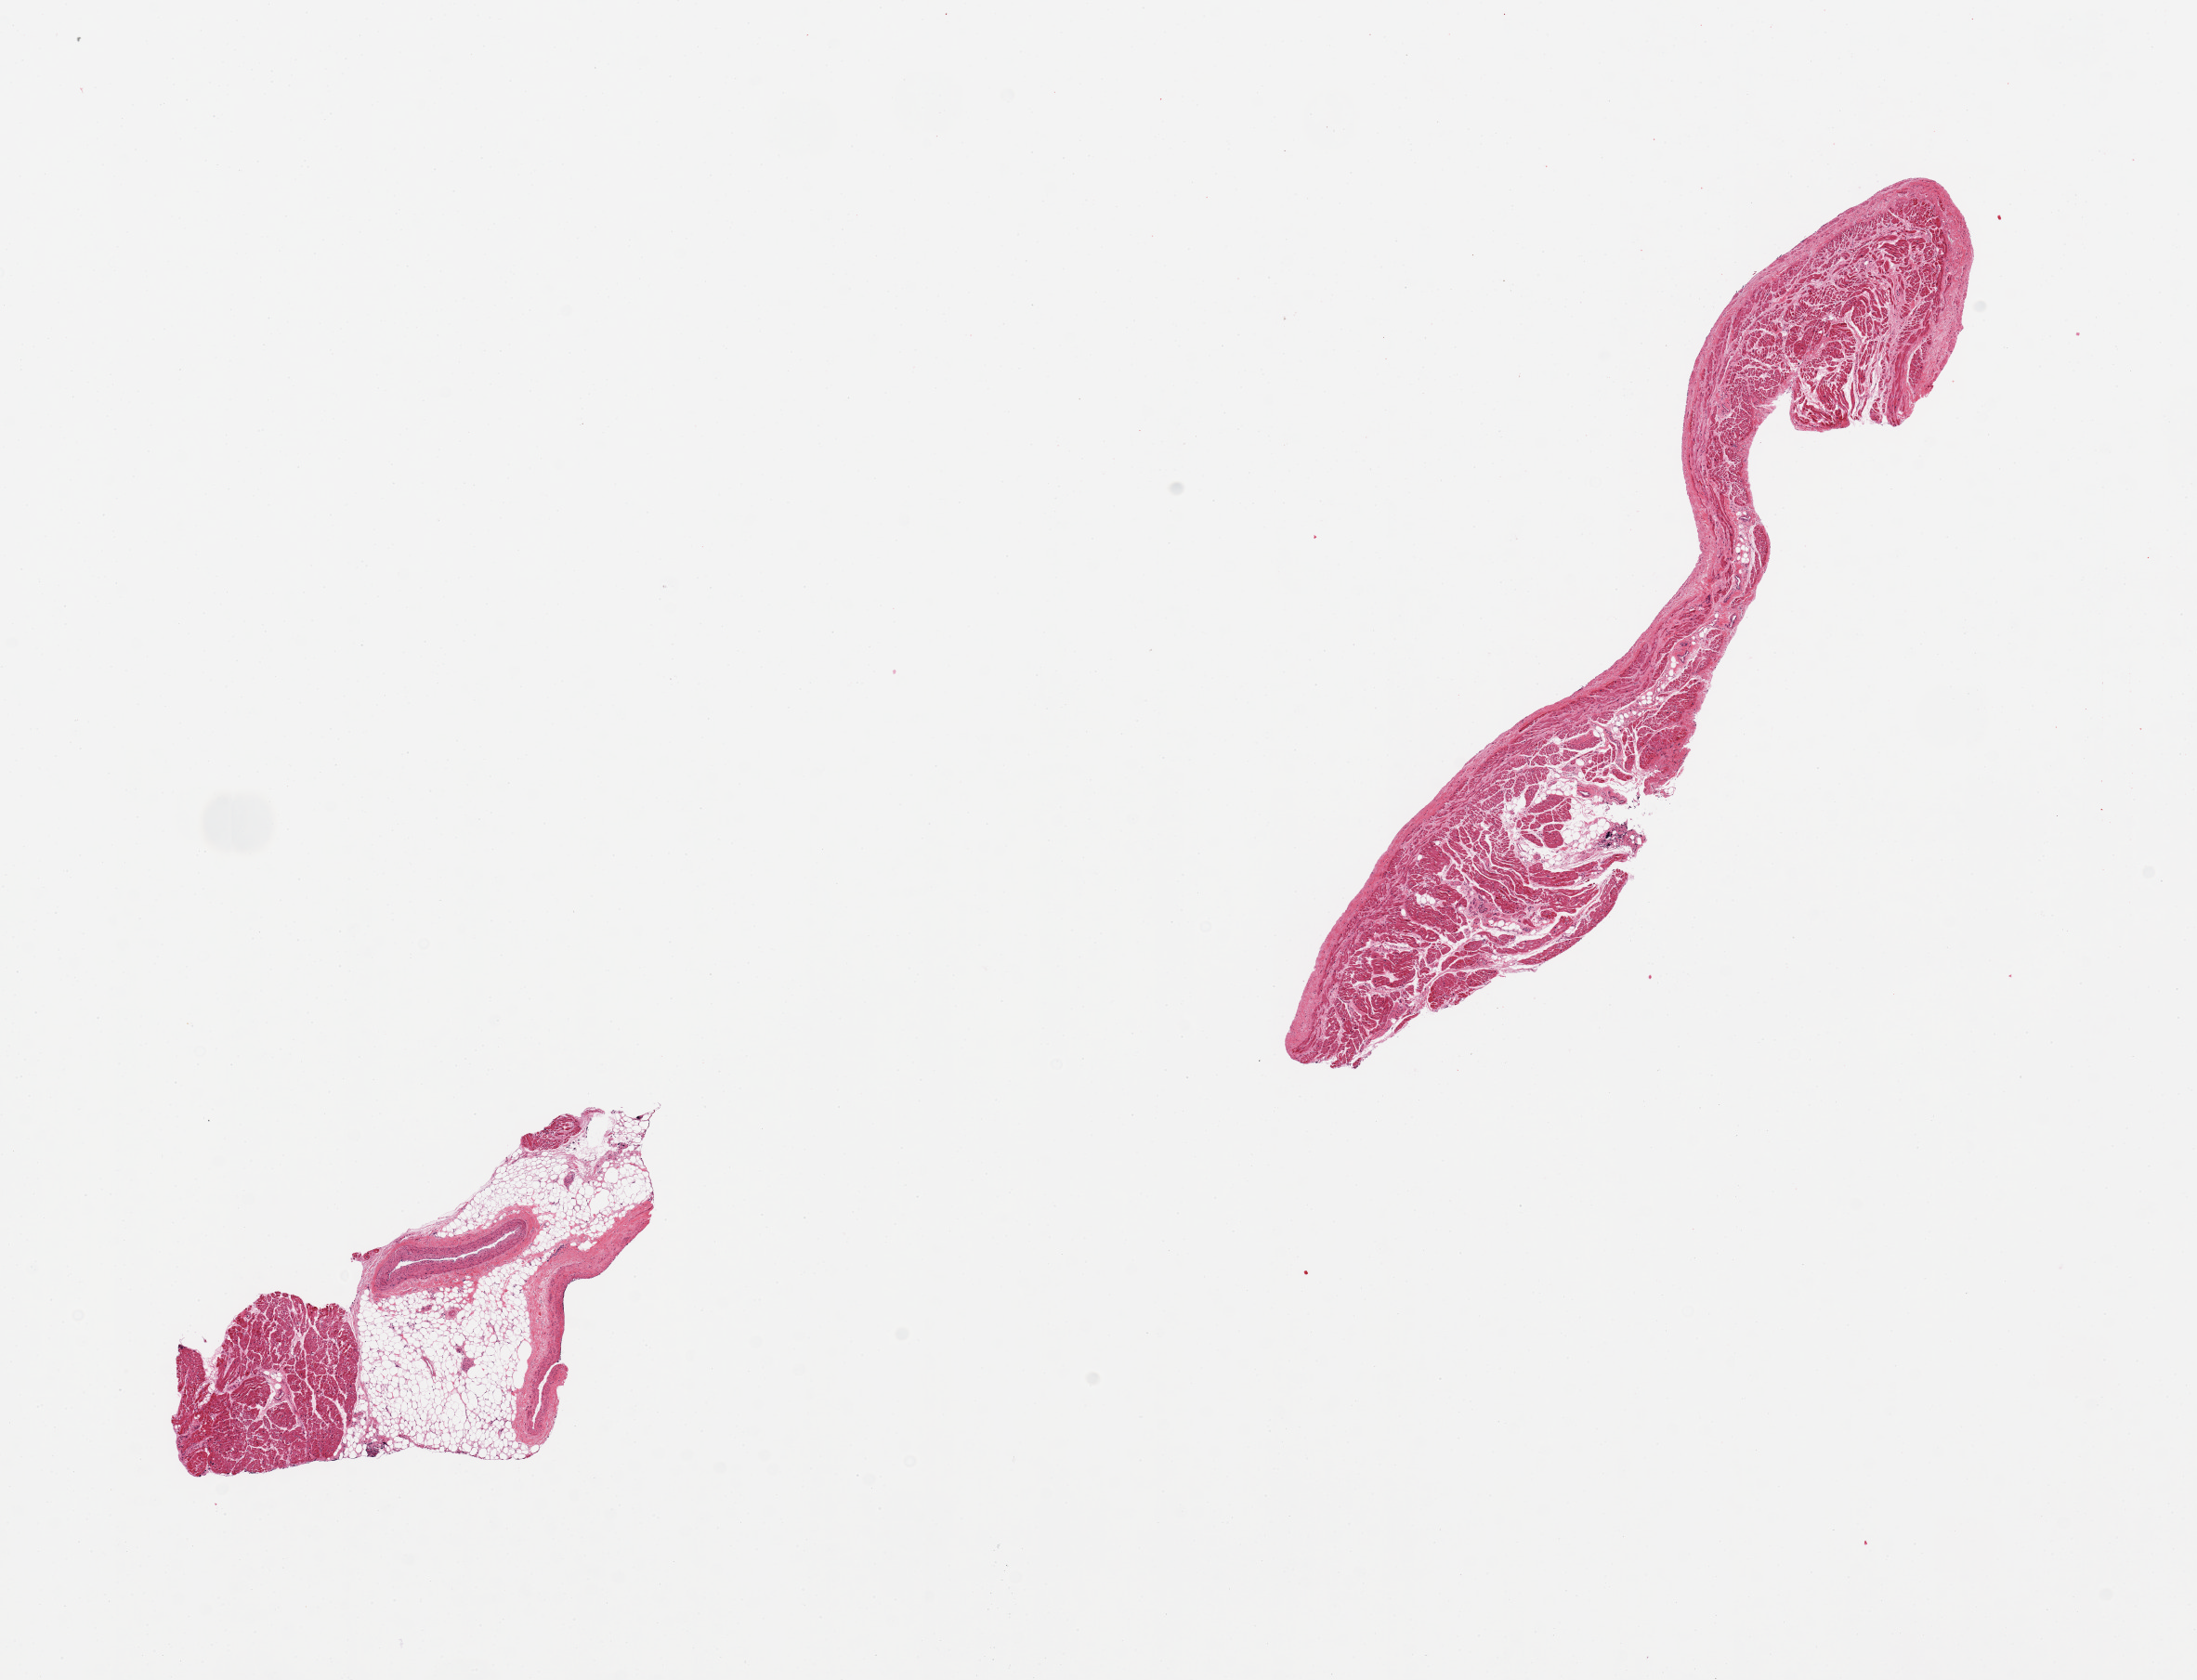
Digitized H&E-stained section, brightfield, low-resolution overview of the scanned area, about 18.7 x 14.3 mm (acquisition: 20x scan). Donor sex: female.
Specimen: PAXgene-fixed, paraffin-embedded tissue; sampled site (target tissue): coronary artery; donor tissue sample.